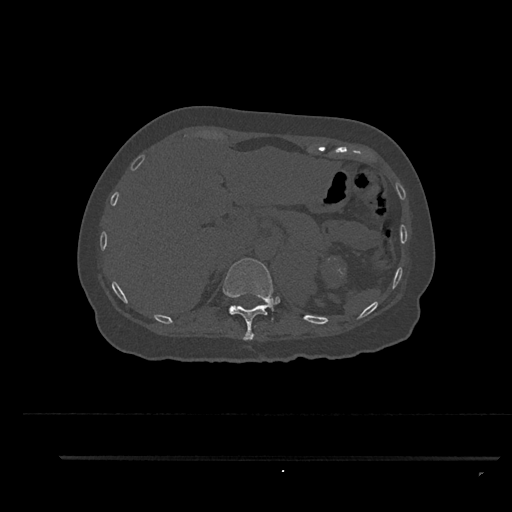
CT including the spine, one axial slice; position 310 of 797 along the scan axis; reconstruction kernel Br40s/3; 120 kVp; bone window (W 1800 / L 400 HU); 0.5 mm slice thickness; 512 × 512 image matrix. Female patient, age 44 years. Case-level facts recorded for this patient, not image findings: primary cancer: renal; vertebrae with lytic lesions (as recorded): L1.
Annotated regions visible in this slice (semi-automatically segmented with operator editing):
- T11 vertebra: bounding box <223,258,274,340> (left, top, right, bottom; pixels)